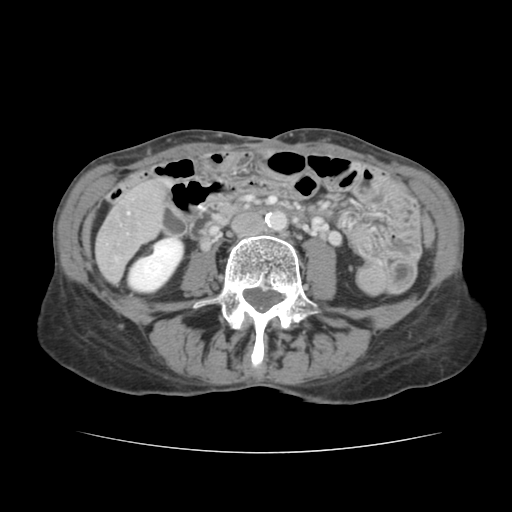
Contrast-enhanced abdominal CT, one axial slice. Slice 26 of 136 in the series (ordered by position). Intravenous contrast given. Soft-tissue window (W 400 / L 40 HU). 512 × 512 image matrix, field of view 319 × 319 mm. Female patient, age 77 years. From the clinical record (not read from this slice): diagnosis: colorectal cancer liver metastases, imaged before liver resection; multiple liver metastases: yes; largest metastasis: 3 cm; disease in both lobes: no.
Outlined on this slice (manually delineated by an expert):
- liver: box from (x=97, y=181) to (x=165, y=280) px